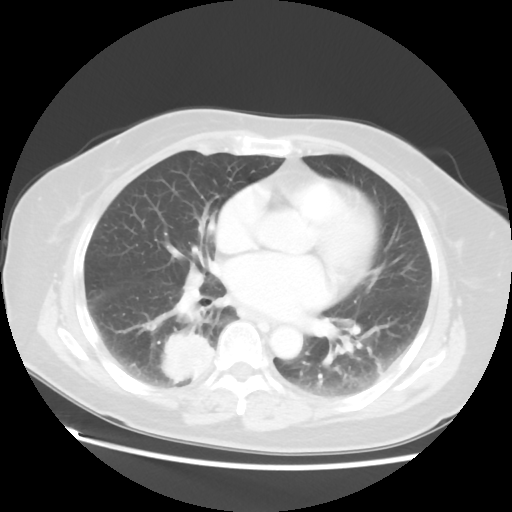
Chest CT, one axial slice. Slice 27 of 52 in the series (ordered by position). Reconstruction kernel STANDARD. 120 kVp. Lung window (W 1500 / L -600 HU). 5 mm slice thickness. 512 × 512 image matrix. Patient: female, 69 years. Case-level facts recorded for this patient, not image findings: clinical TNM (as recorded): T2 N1 M1a.
Outlined on this slice (bounding box drawn by a radiologist):
- lung tumour (recorded histology: adenocarcinoma): box from (x=154, y=330) to (x=219, y=389) px